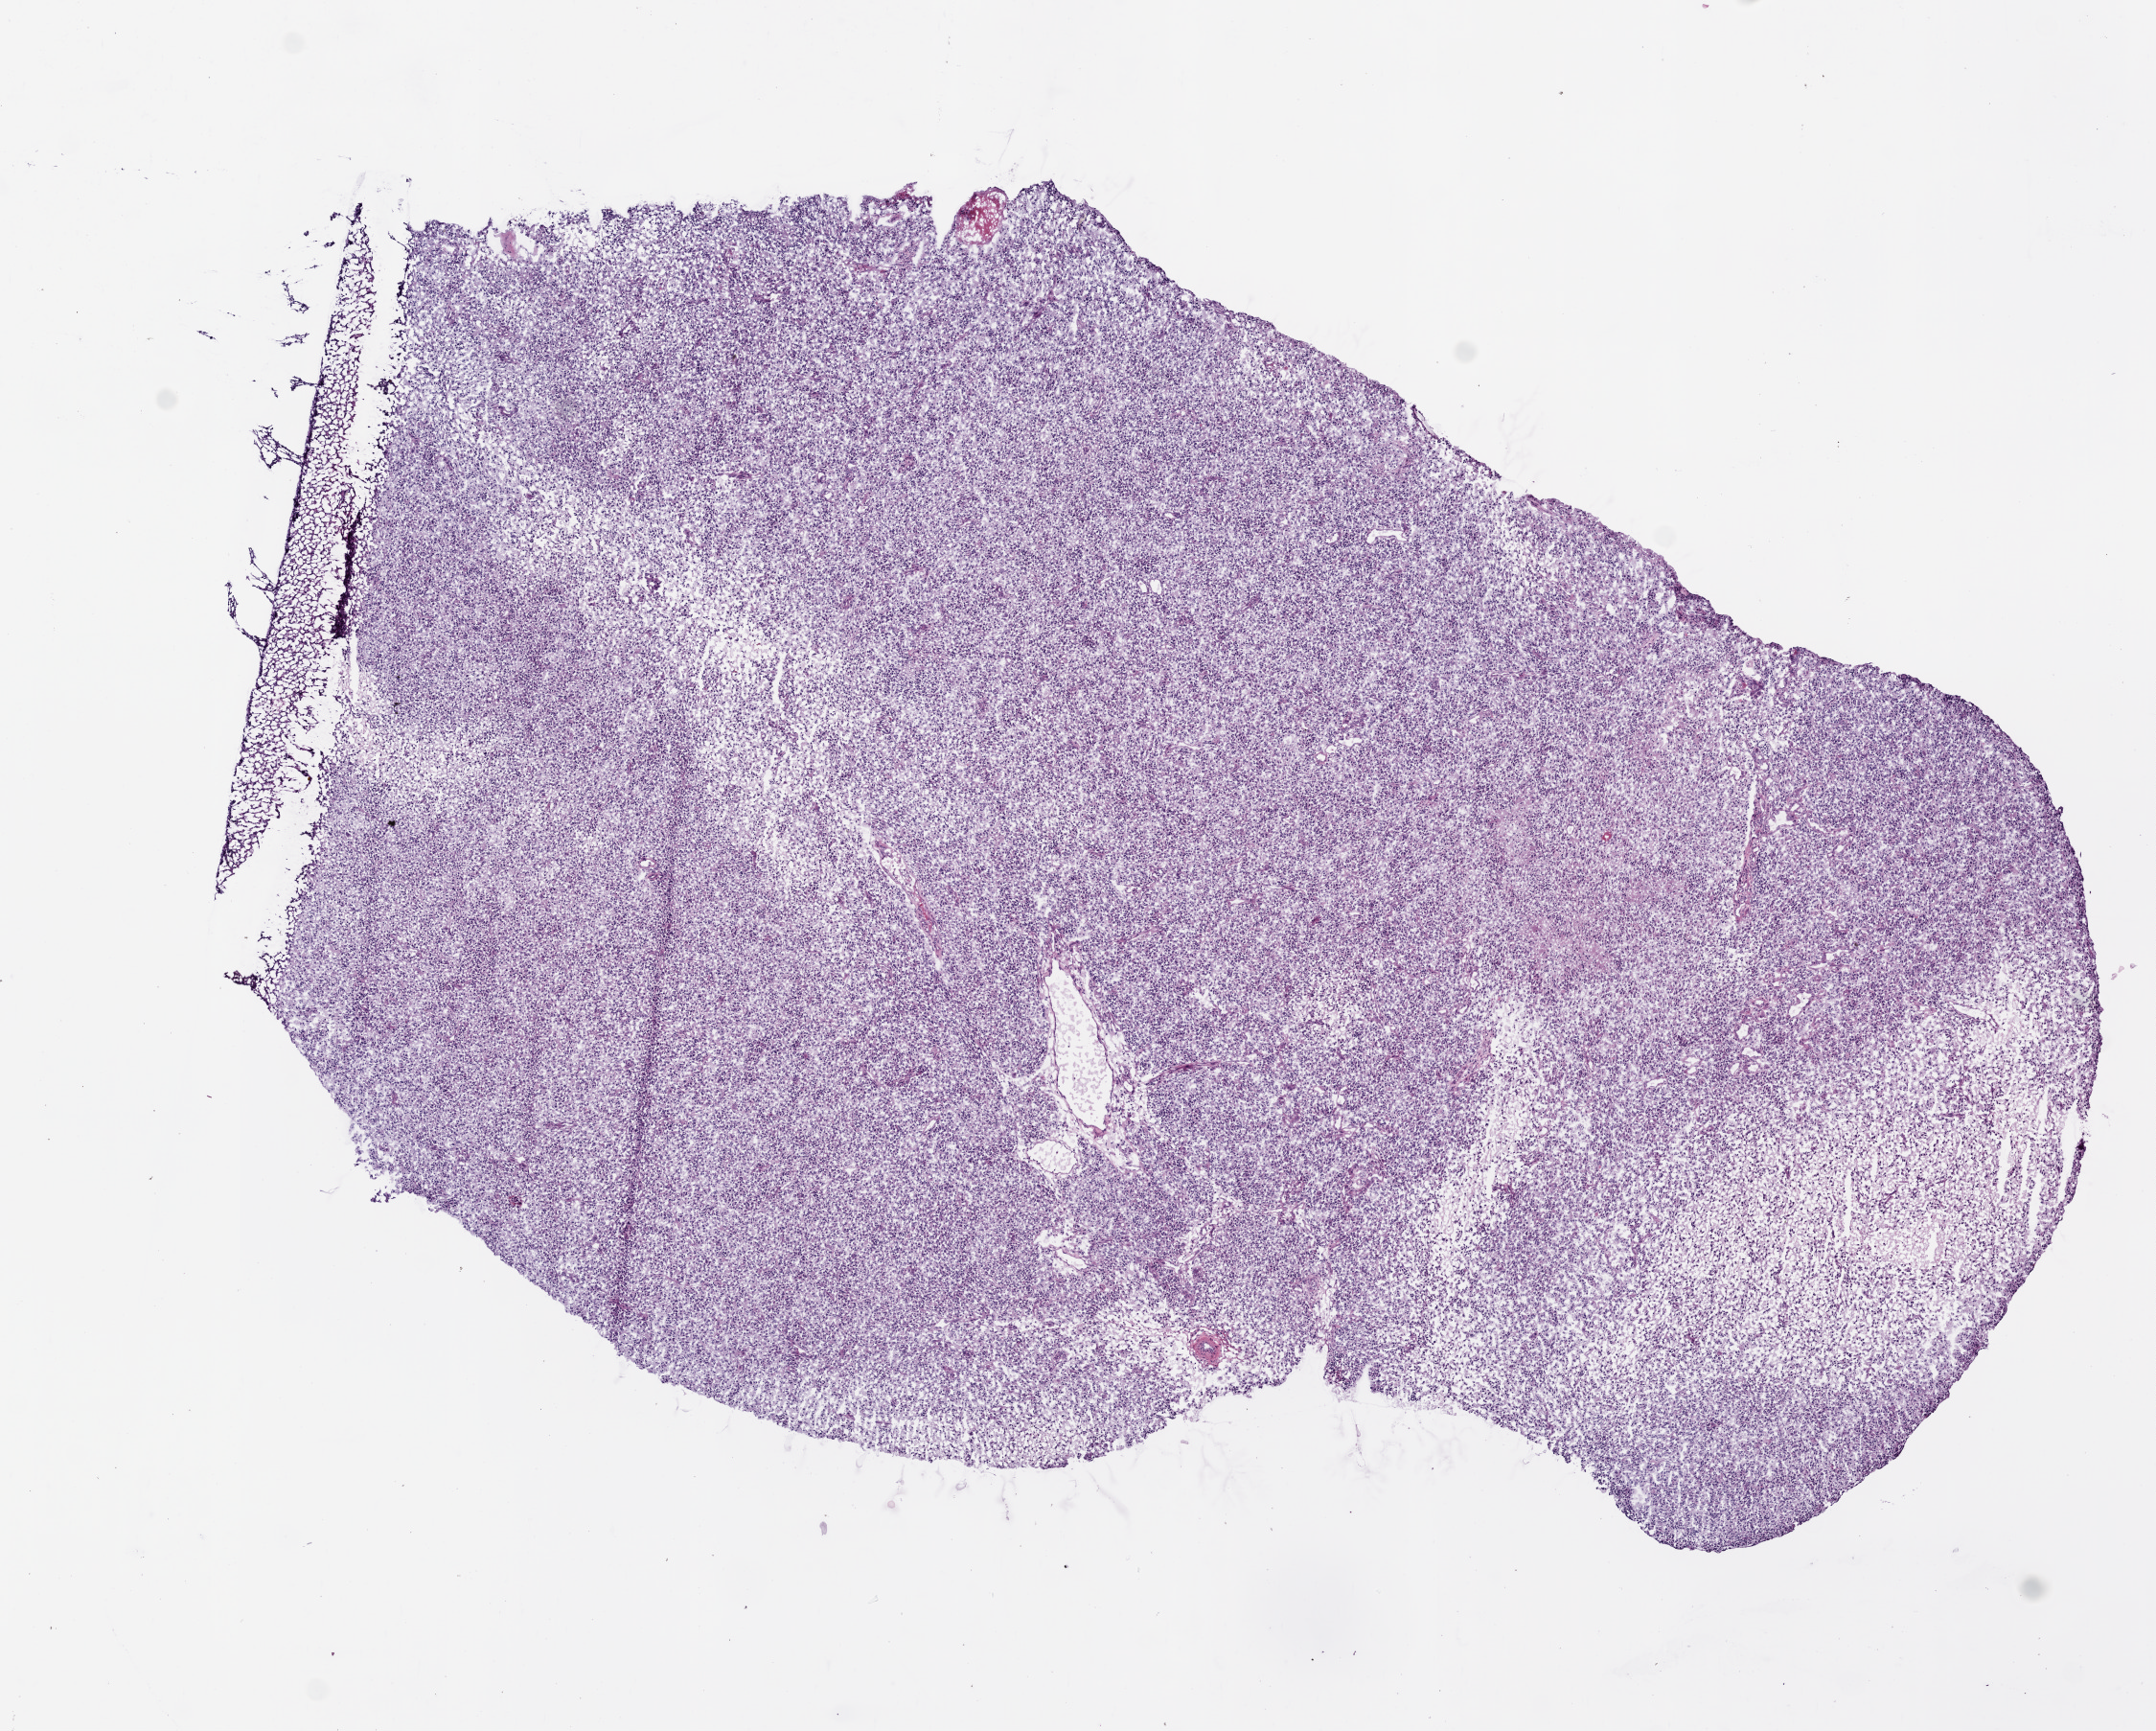
Digitized H&E-stained tissue section (whole slide), a low-resolution overview of the entire scanned area, about 9.0 x 7.2 mm; frozen section from the bottom of the tissue portion; primary tumour sample from the brain. Male patient; age at initial diagnosis 72 years. Composition of this section per pathologist review: tumour cells 90%, tumour nuclei 85%, normal cells 0%, stromal cells 0%, necrosis 10%.
- histologic diagnosis: Glioblastoma